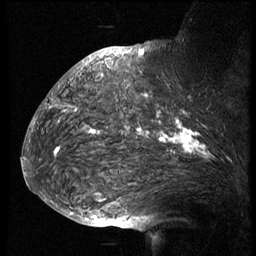
Breast MRI (dynamic contrast-enhanced), one sagittal slice; slice 47 of 74 in the series (ordered by position); 3 images stored at this slice position (order not interpretable as contrast timing); 1.5 T; TE 4.2 ms, TR 8.9 ms; 2.5 mm slice thickness; 256 × 256 image matrix. Female patient, age 57 years. From the clinical record (not read from this slice): setting: breast cancer imaged before/during neoadjuvant chemotherapy; receptor status: HER2-positive.
Annotated regions visible in this slice (semi-automatic segmentation, software-assisted and operator-edited):
- analysis volume of interest (the breast-tissue region the enhancement analysis was run in; not a lesion): bounding box [x1, y1, x2, y2] px = [51, 67, 248, 173]
- tumour enhancement mask (voxels above the 140 % enhancement threshold inside the analysis volume of interest): [56, 113, 210, 156]